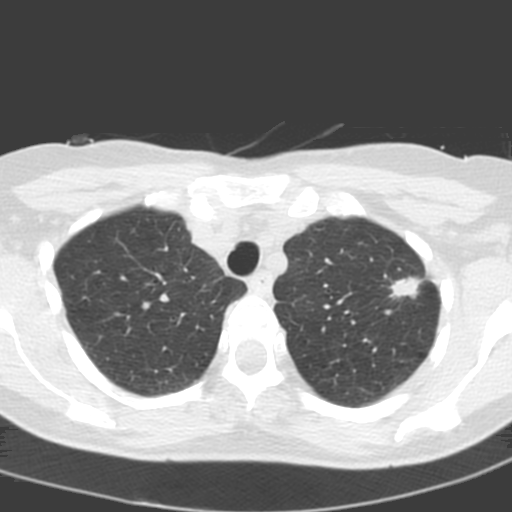
Low-dose screening chest CT, one axial slice; slice 157 of 193 in the series (ordered by position); lung window (W 1500 / L -600 HU); 3.2 mm slice thickness; 512 × 512 image matrix.
Annotated regions visible in this slice (outlined manually by an expert reader):
- lesion 1 (tumor, upper lobe of left lung): bounding box [x1, y1, x2, y2] px = [390, 277, 421, 298]